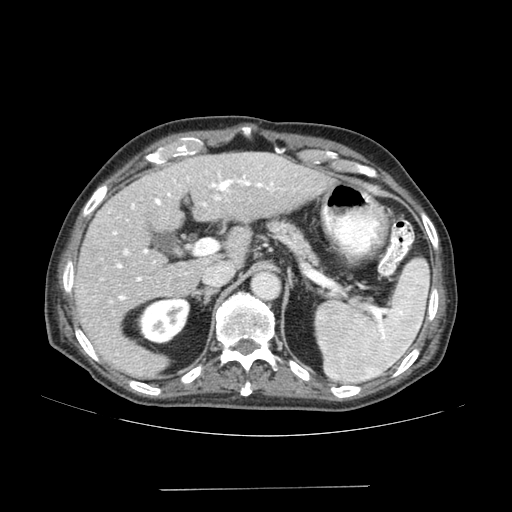
Contrast-enhanced abdominal CT (liver protocol), one axial slice; position 104 of 192 along the scan axis; reconstruction kernel SOFT; 120 kVp; soft-tissue window (W 400 / L 40 HU); 512 × 512 image matrix. Case-level facts recorded for this patient, not image findings: diagnosis: hepatocellular carcinoma (patient treated with transarterial chemoembolisation; whether this scan precedes or follows treatment is not stated here); TNM stage (as recorded): Stage-IVA; Child-Pugh class: A; tumour differentiation: poorly differentiated; tumour nodularity: uninodular.
Structures marked on this image (semi-automatically segmented with operator editing):
- liver parenchyma outside the tumour (the mass and vessels are separate outlines, so this box may not span the whole liver): bounding box <74,152,330,378> (left, top, right, bottom; pixels)
- liver vessels: <110,173,274,302>